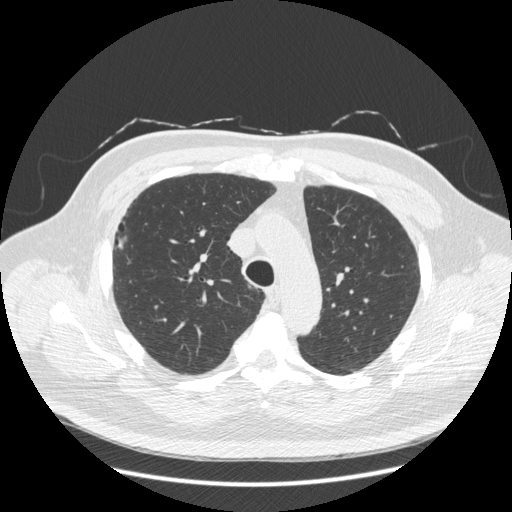
Low-dose screening chest CT, axial slice. Second annual screen. Lung window (W 1500 / L -600 HU). 120 kVp. 512 × 512 image matrix, field of view 400 × 400 mm. Male, age 66 years at enrolment. Current smoker at enrolment.
Expert-annotated lung lesion, bounding box (x1, y1, x2, y2) in pixels: (101, 213, 142, 264). The screening reader recorded 2 non-calcified nodules or masses ≥4 mm on this exam (right lower lobe, right lower lobe); which of them this box marks is not recorded. Participant outcome: lung cancer diagnosed 403 days after this screen (after the third annual screen) — non-small cell carcinoma, right upper lobe, stage IV (AJCC 6th edition), 50 mm at pathology.